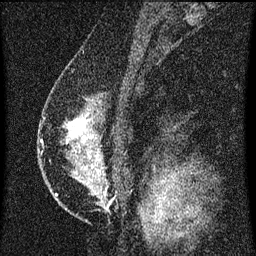
Breast MRI (dynamic contrast-enhanced), one sagittal slice; position 38 of 60 along the scan axis; dynamic contrast-enhanced series, image 2 of 3 at this slice position (ordered by acquisition); 1.5 T; TE 4.2 ms, TR 8 ms; 256 × 256 image matrix. Female patient, age 47 years.
Structures marked on this image (semi-automatically segmented with operator editing):
- analysis volume of interest (the breast-tissue region the enhancement analysis was run in; not a lesion): bounding box (x1, y1, x2, y2) in pixels: (50, 90, 124, 203)
- tumour enhancement mask (voxels above the 70 % enhancement threshold inside the analysis volume of interest): (69, 120, 87, 137)